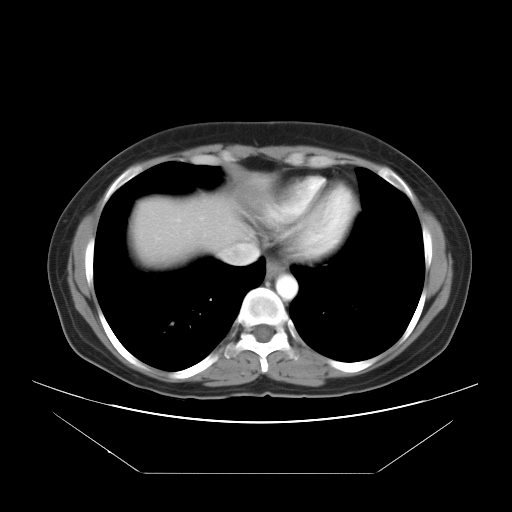
Contrast-enhanced abdominal CT, one axial slice; slice 33 of 34 in the series (ordered by position); 120 kVp; intravenous contrast given; soft-tissue window (W 400 / L 40 HU); 7.5 mm slice thickness; 512 × 512 image matrix, field of view 410 × 410 mm. Female patient, age 38 years. Case-level facts recorded for this patient, not image findings: diagnosis: colorectal cancer liver metastases, imaged before liver resection; multiple liver metastases: yes; largest metastasis: 3.1 cm; disease in both lobes: no.
Structures marked on this image (outlined manually by an expert reader):
- liver: bounding box (x1, y1, x2, y2) in pixels: (126, 193, 254, 270)
- planned liver remnant (the part of the liver to remain after resection): (208, 193, 255, 249)